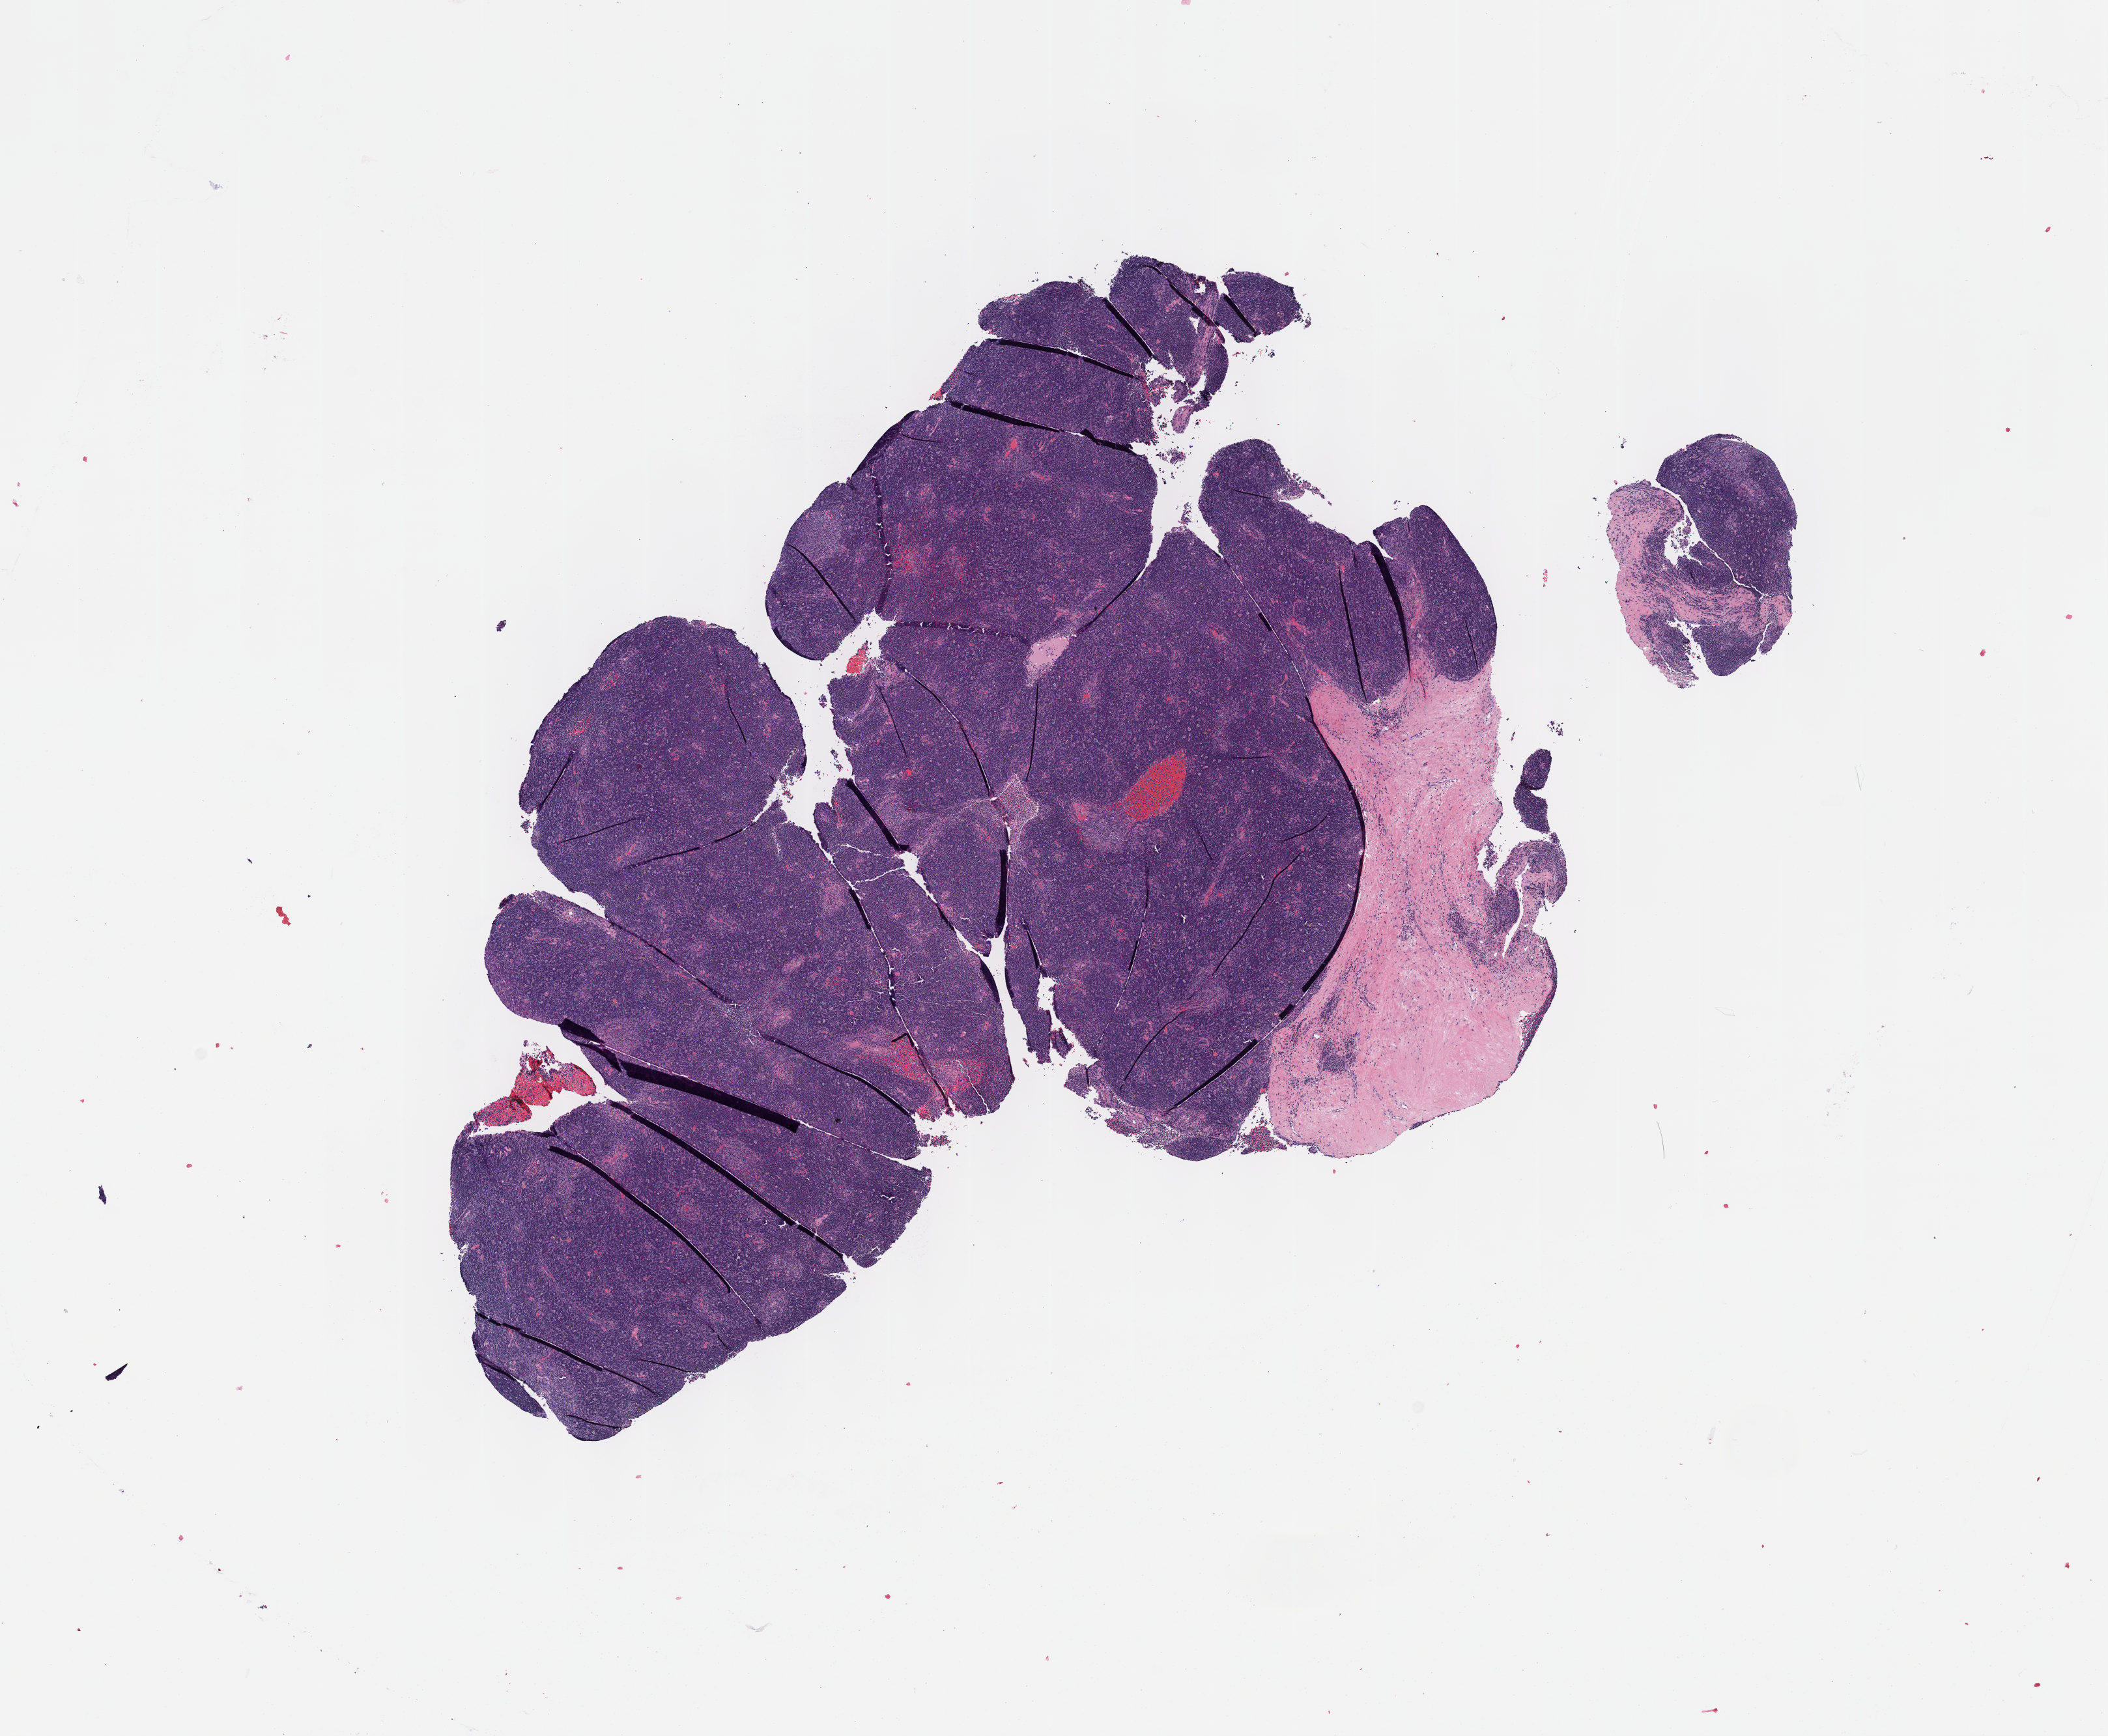
H&E whole-slide image, whole scanned area (about 13.1 x 10.8 mm, slide scanned at 40x) shown as a low-resolution overview, formalin-fixed paraffin-embedded (FFPE) diagnostic section, sample: primary tumour, thymus. Patient: male, age at initial diagnosis 47 years.
Pathologic diagnosis: Thymoma, type B2, NOS.